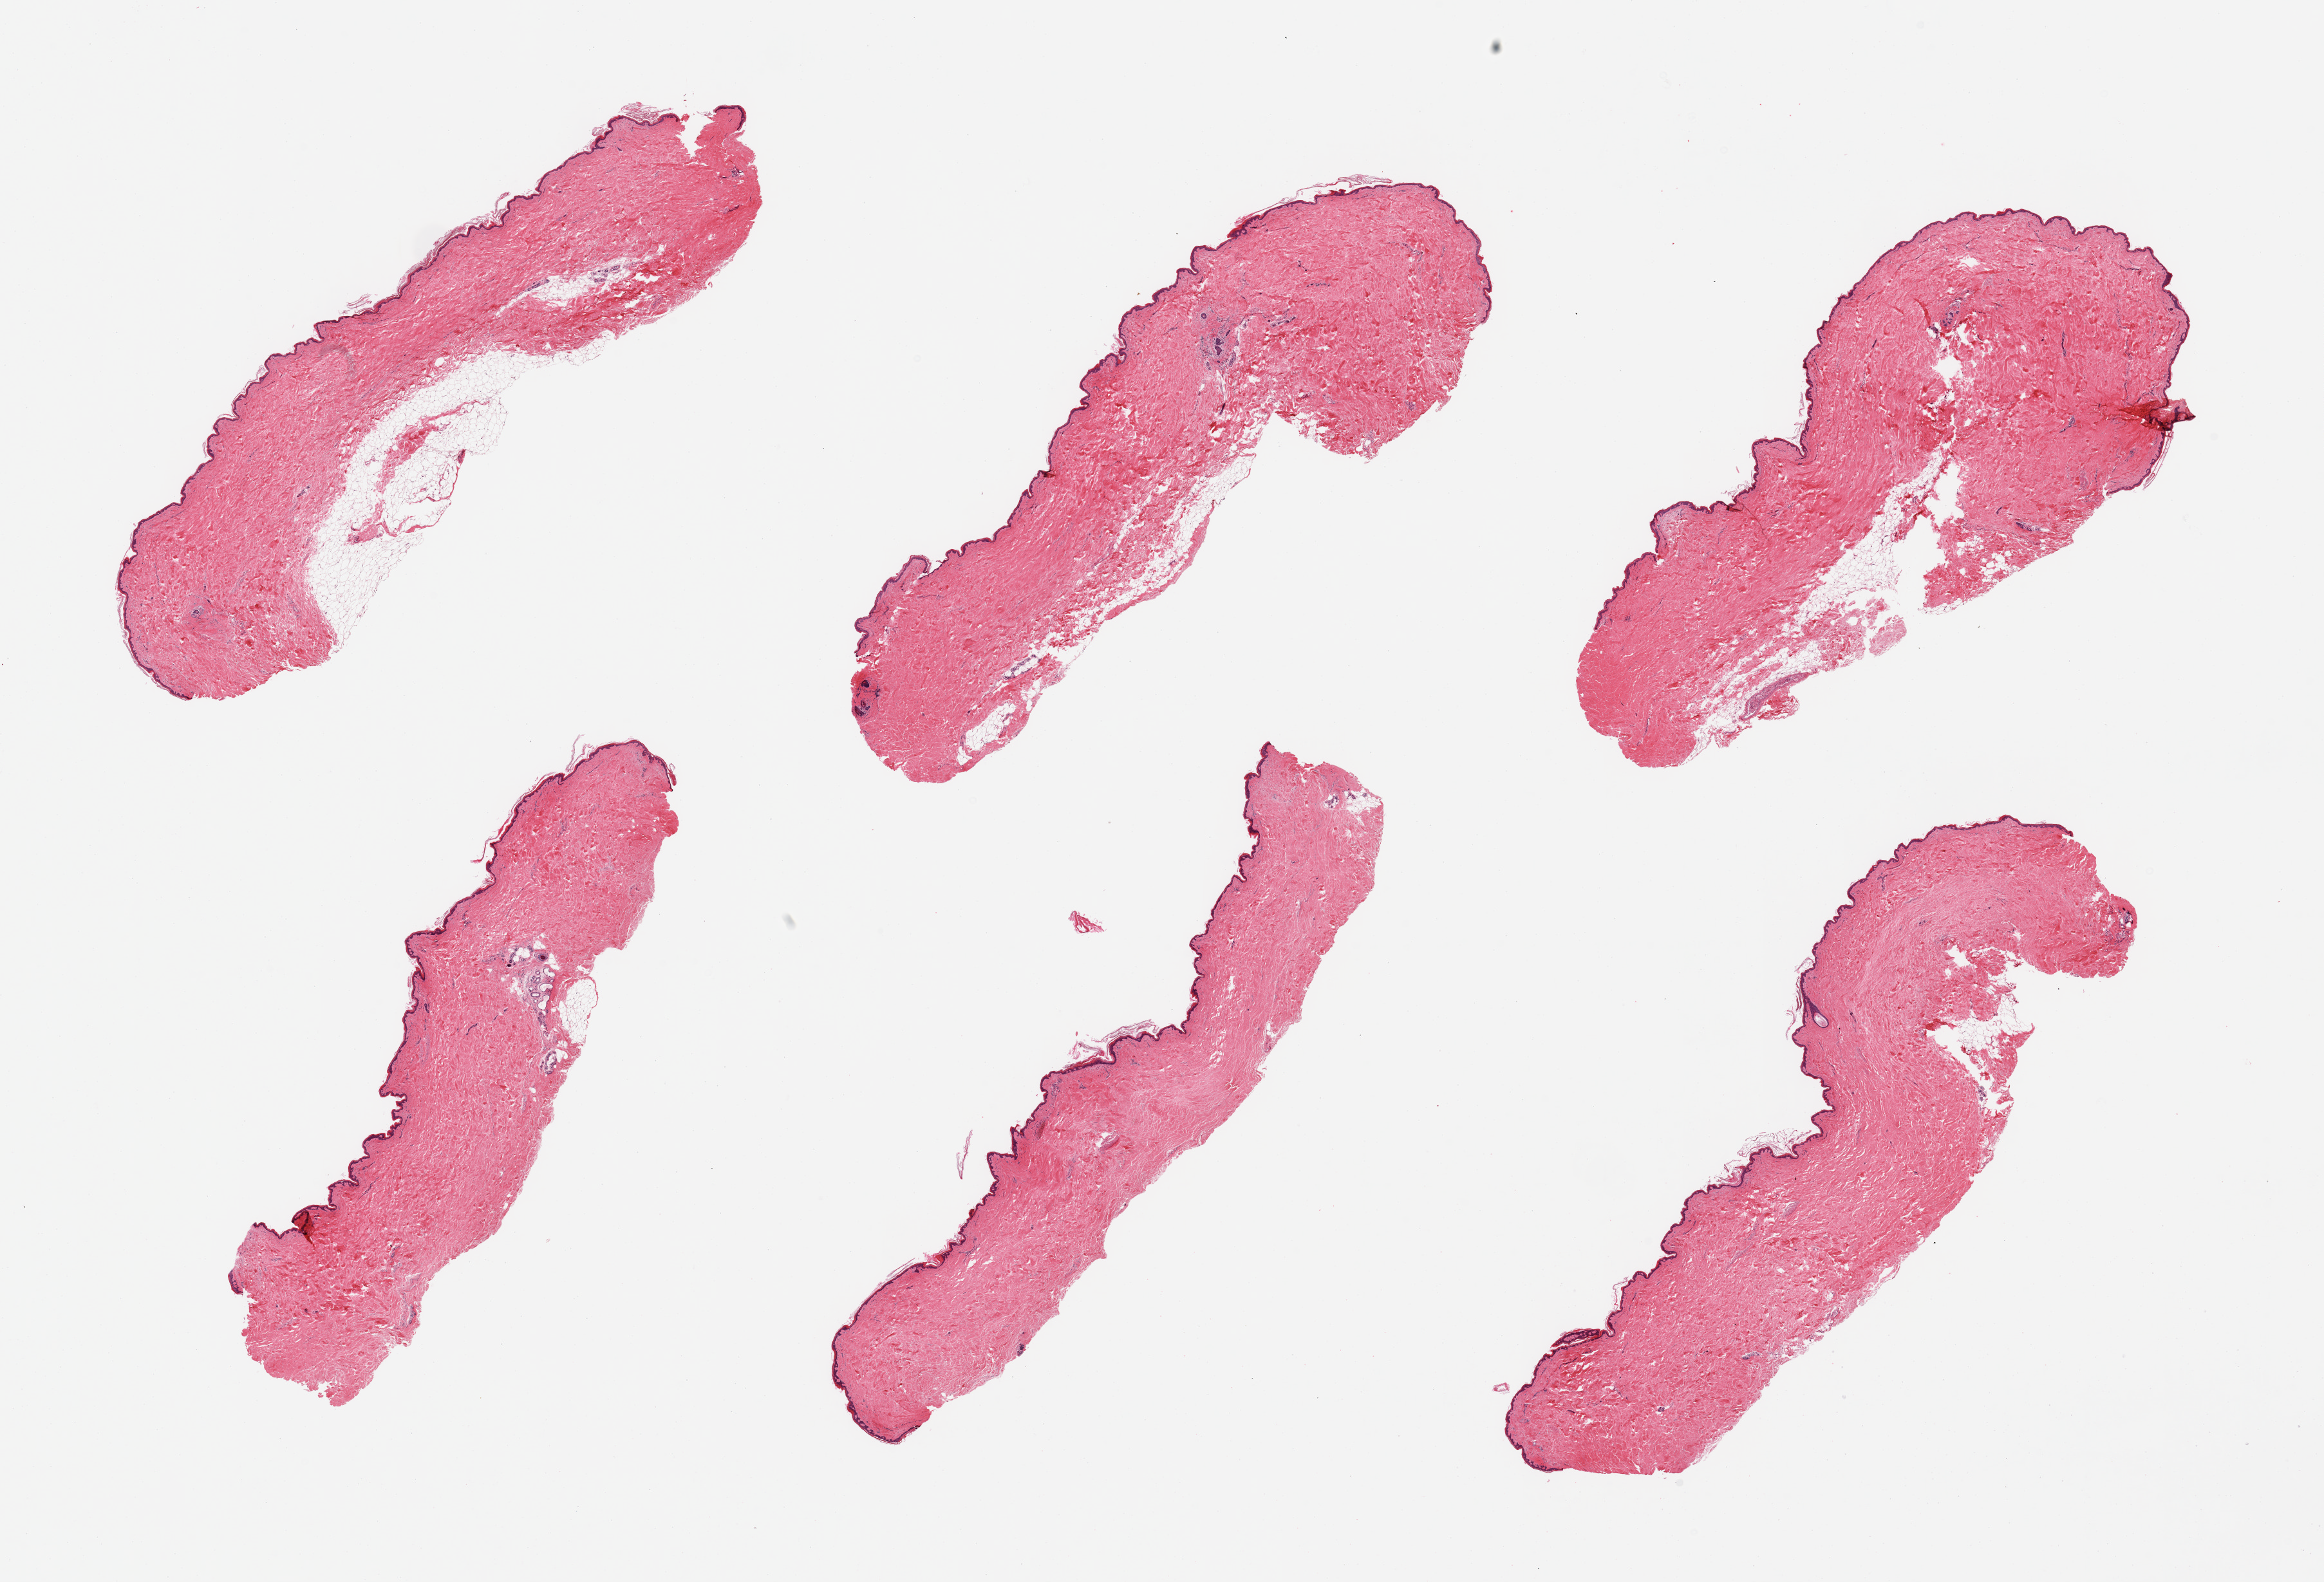
Digitized H&E-stained section — a low-resolution overview of the entire scanned area, about 28.5 x 19.4 mm; PAXgene-fixed, paraffin-embedded tissue; sampled site (target tissue): skin of suprapubic region; donor tissue sample. Donor: female.
Review note (as recorded): 6 pieces, trace adherent dermal fat, up to ~1mm.